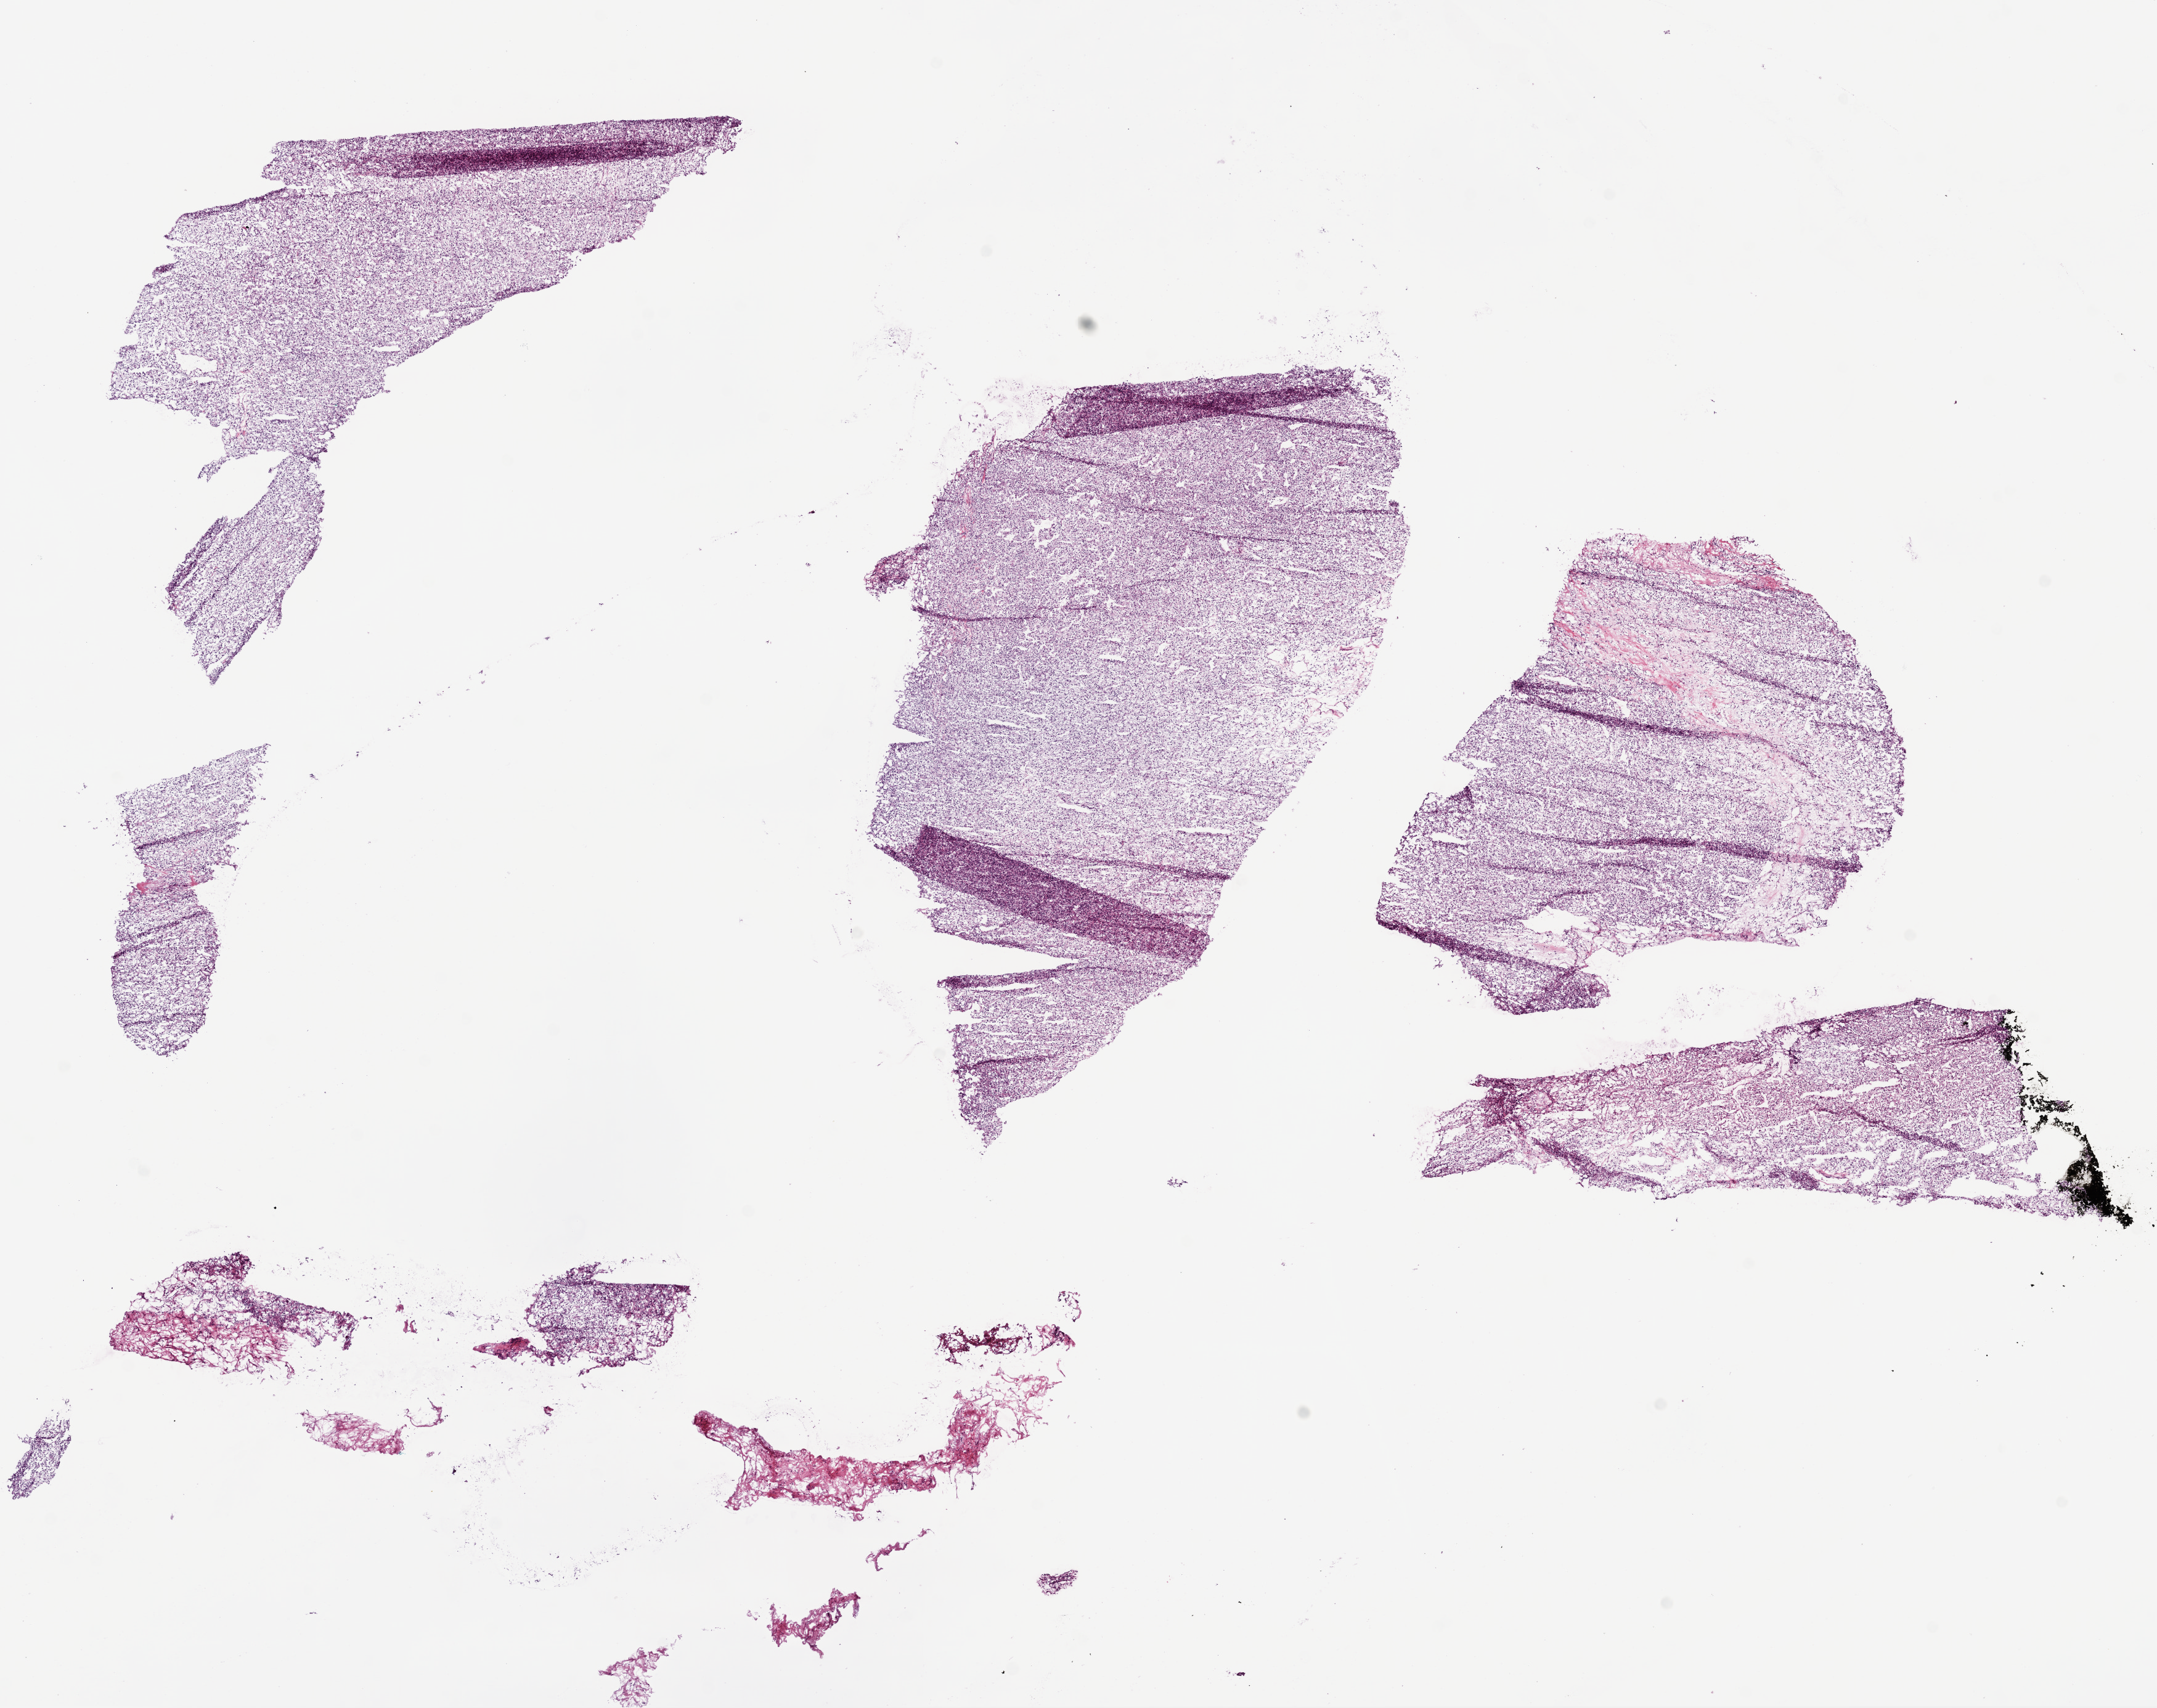
Digitized H&E tissue section (whole slide) — a low-resolution overview of the entire scanned area, about 14.0 x 11.1 mm (acquisition: 20x scan), frozen section from the bottom of the tissue portion, kidney, primary tumour sample. Male, age 52 years at initial diagnosis. Histologic grade: G2 (moderately differentiated). Pathologist review of this section (percent, as recorded): tumour cells 95%, tumour nuclei 85%, normal cells 0%, stromal cells 5%, necrosis 0%.
Pathologic diagnosis: Clear cell adenocarcinoma, NOS. AJCC pathologic stage: I.